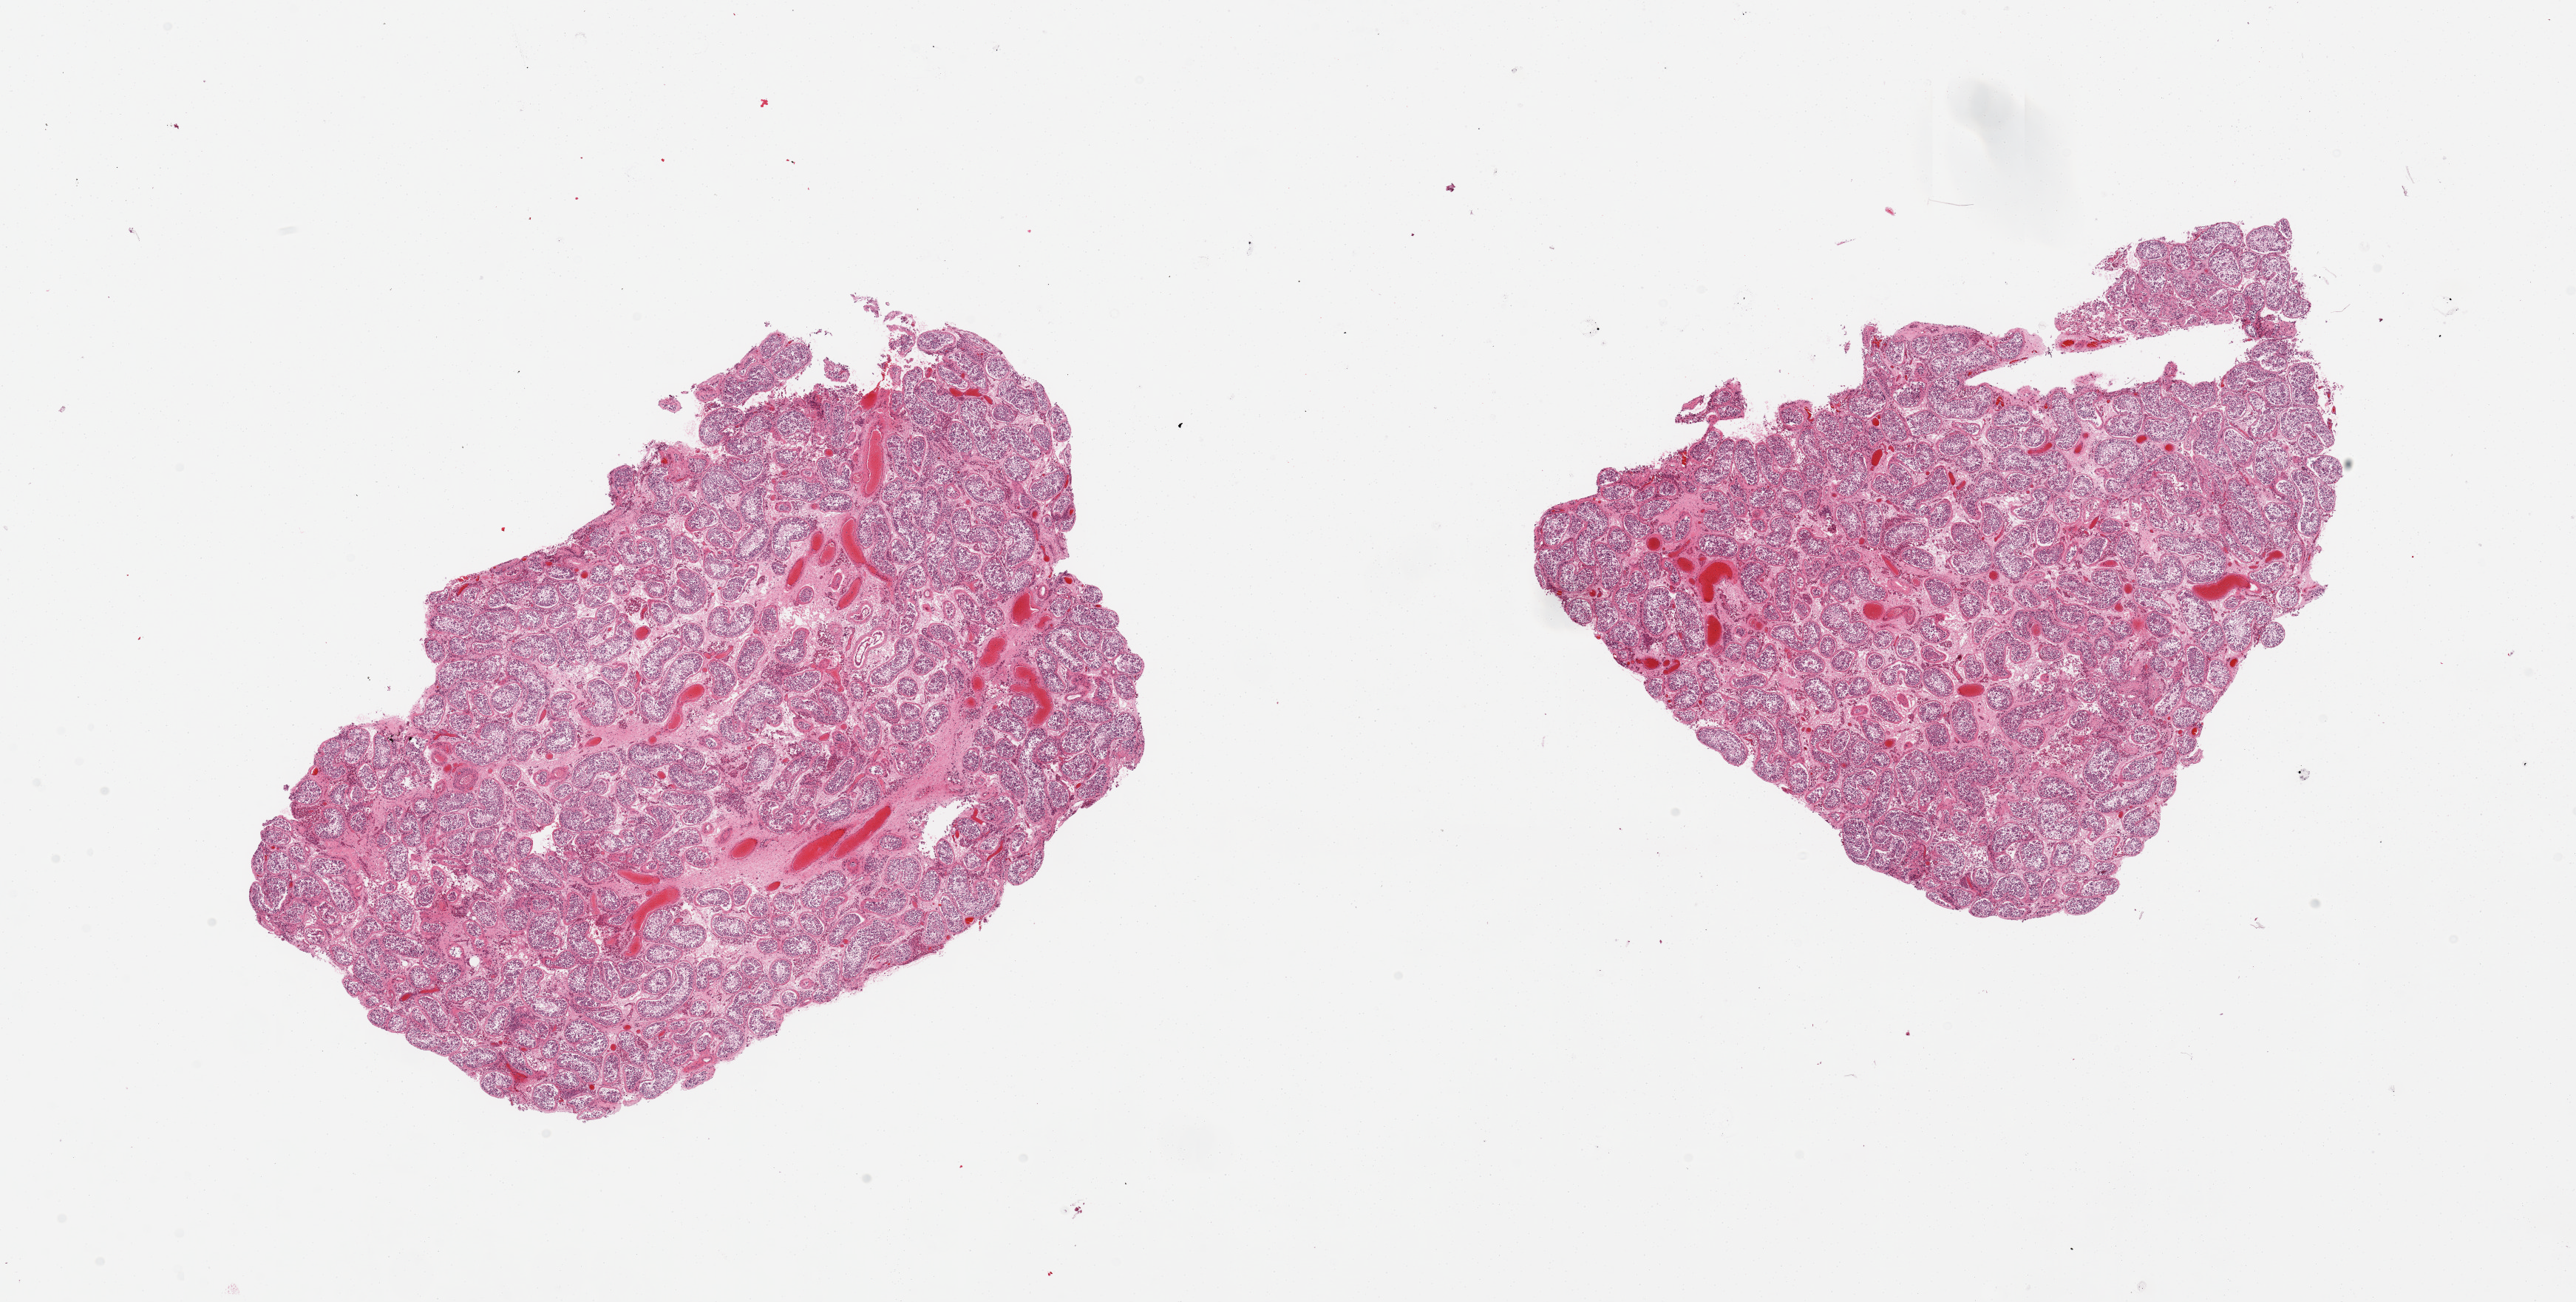
Whole-slide image, H&E stain, a low-resolution overview of the entire scanned area, about 27.6 x 13.9 mm, PAXgene-fixed paraffin-embedded (PFPE) section, target tissue: testis, donor tissue sample.
Reviewer comment on this tissue sample: 2 pieces; Leydig cell hyperplasia.